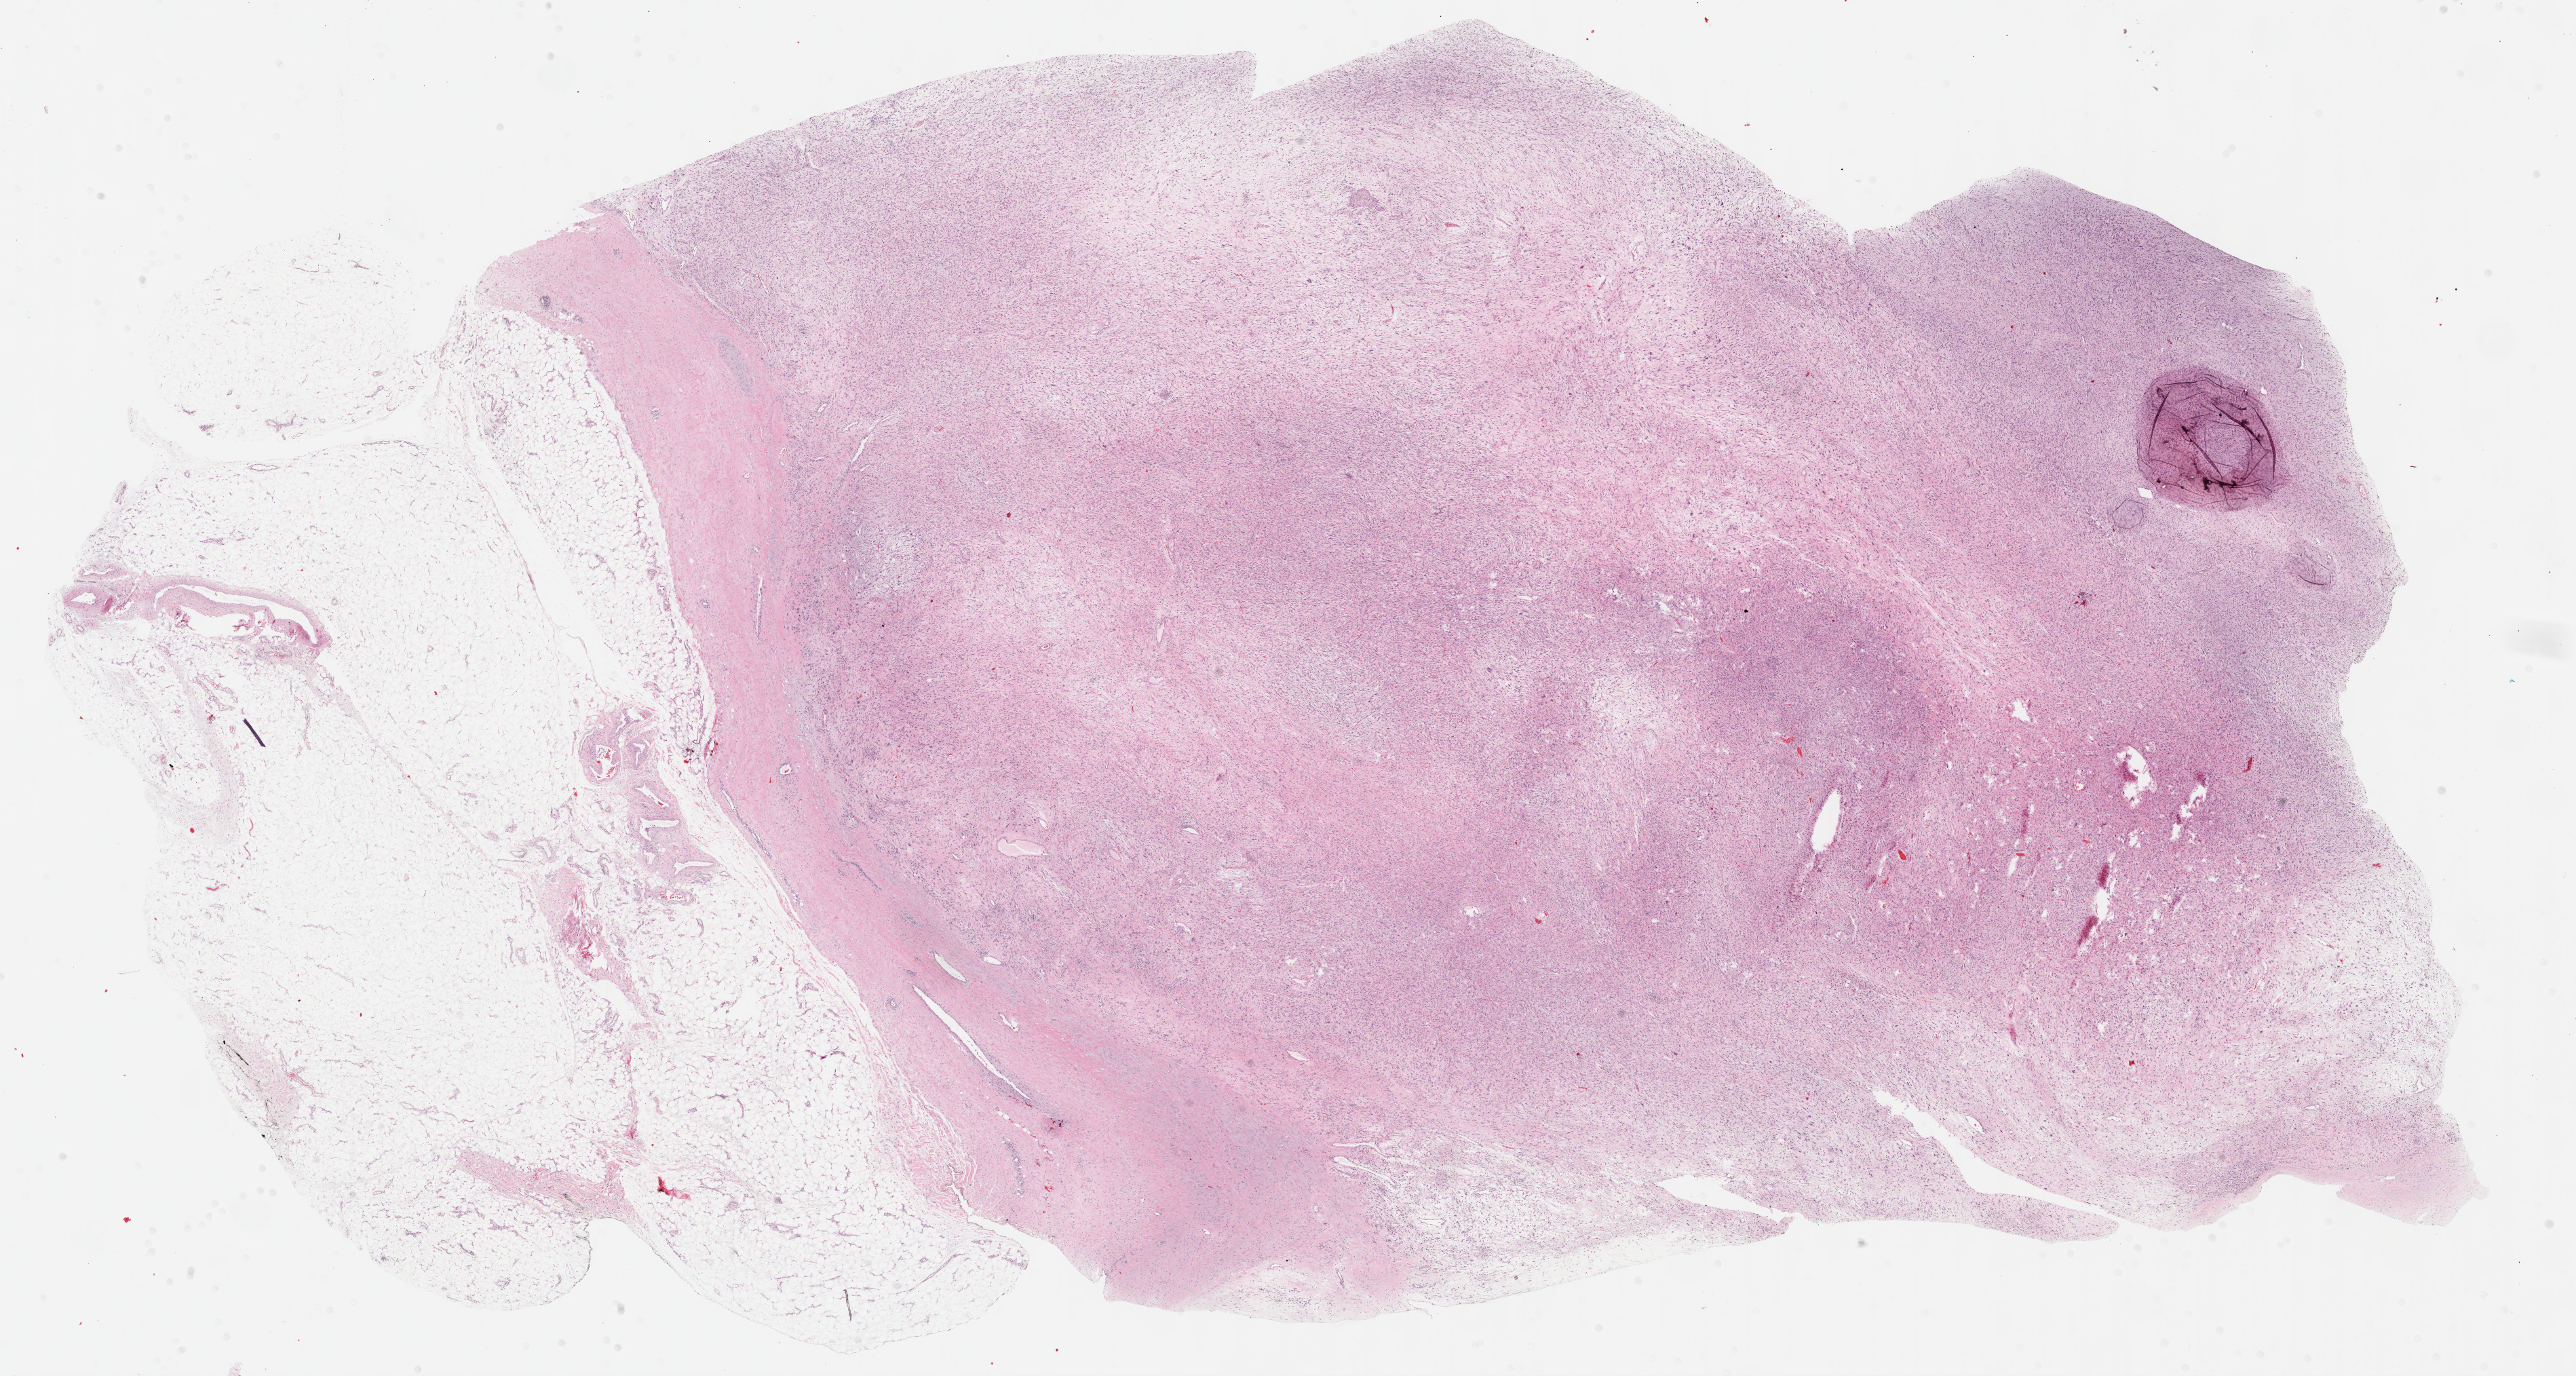
Digitized Hematoxylin and eosin (H&E) stained tissue section (whole slide), shown as a low-resolution overview of the whole scanned area (about 30.7 x 16.4 mm, acquisition: 40x scan); formalin-fixed paraffin-embedded (FFPE) diagnostic section; primary tumour sample from the connective, subcutaneous and other soft tissues. Patient: female, age at initial diagnosis 31 years.
- histologic diagnosis: Fibromyxosarcoma